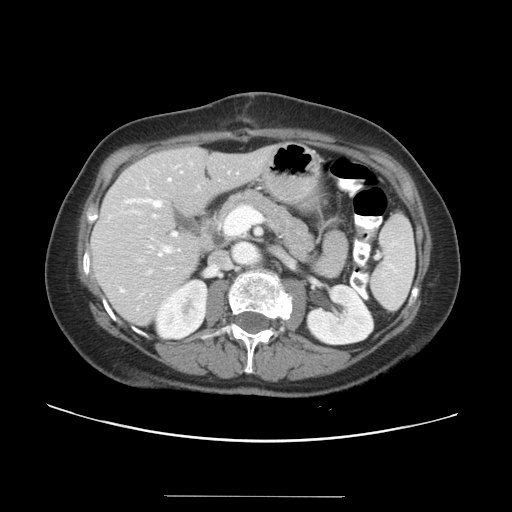
Contrast-enhanced abdominal CT, one axial slice; slice 16 of 34 in the series (ordered by position); reconstruction kernel STANDARD; intravenous contrast given; soft-tissue window (W 400 / L 40 HU); 5 mm slice thickness; 512 × 512 image matrix. Female patient, age 69 years. Case-level facts recorded for this patient, not image findings: diagnosis: colorectal cancer liver metastases, imaged before liver resection; multiple liver metastases: yes; largest metastasis: 1.4 cm; disease in both lobes: yes.
Outlined on this slice (outlined manually by an expert reader):
- hepatic veins: bounding box <125,178,179,273> (left, top, right, bottom; pixels)
- liver: <92,147,276,324>
- planned liver remnant (the part of the liver to remain after resection): <93,147,275,324>
- portal vein (with intrahepatic branches): <159,206,262,255>